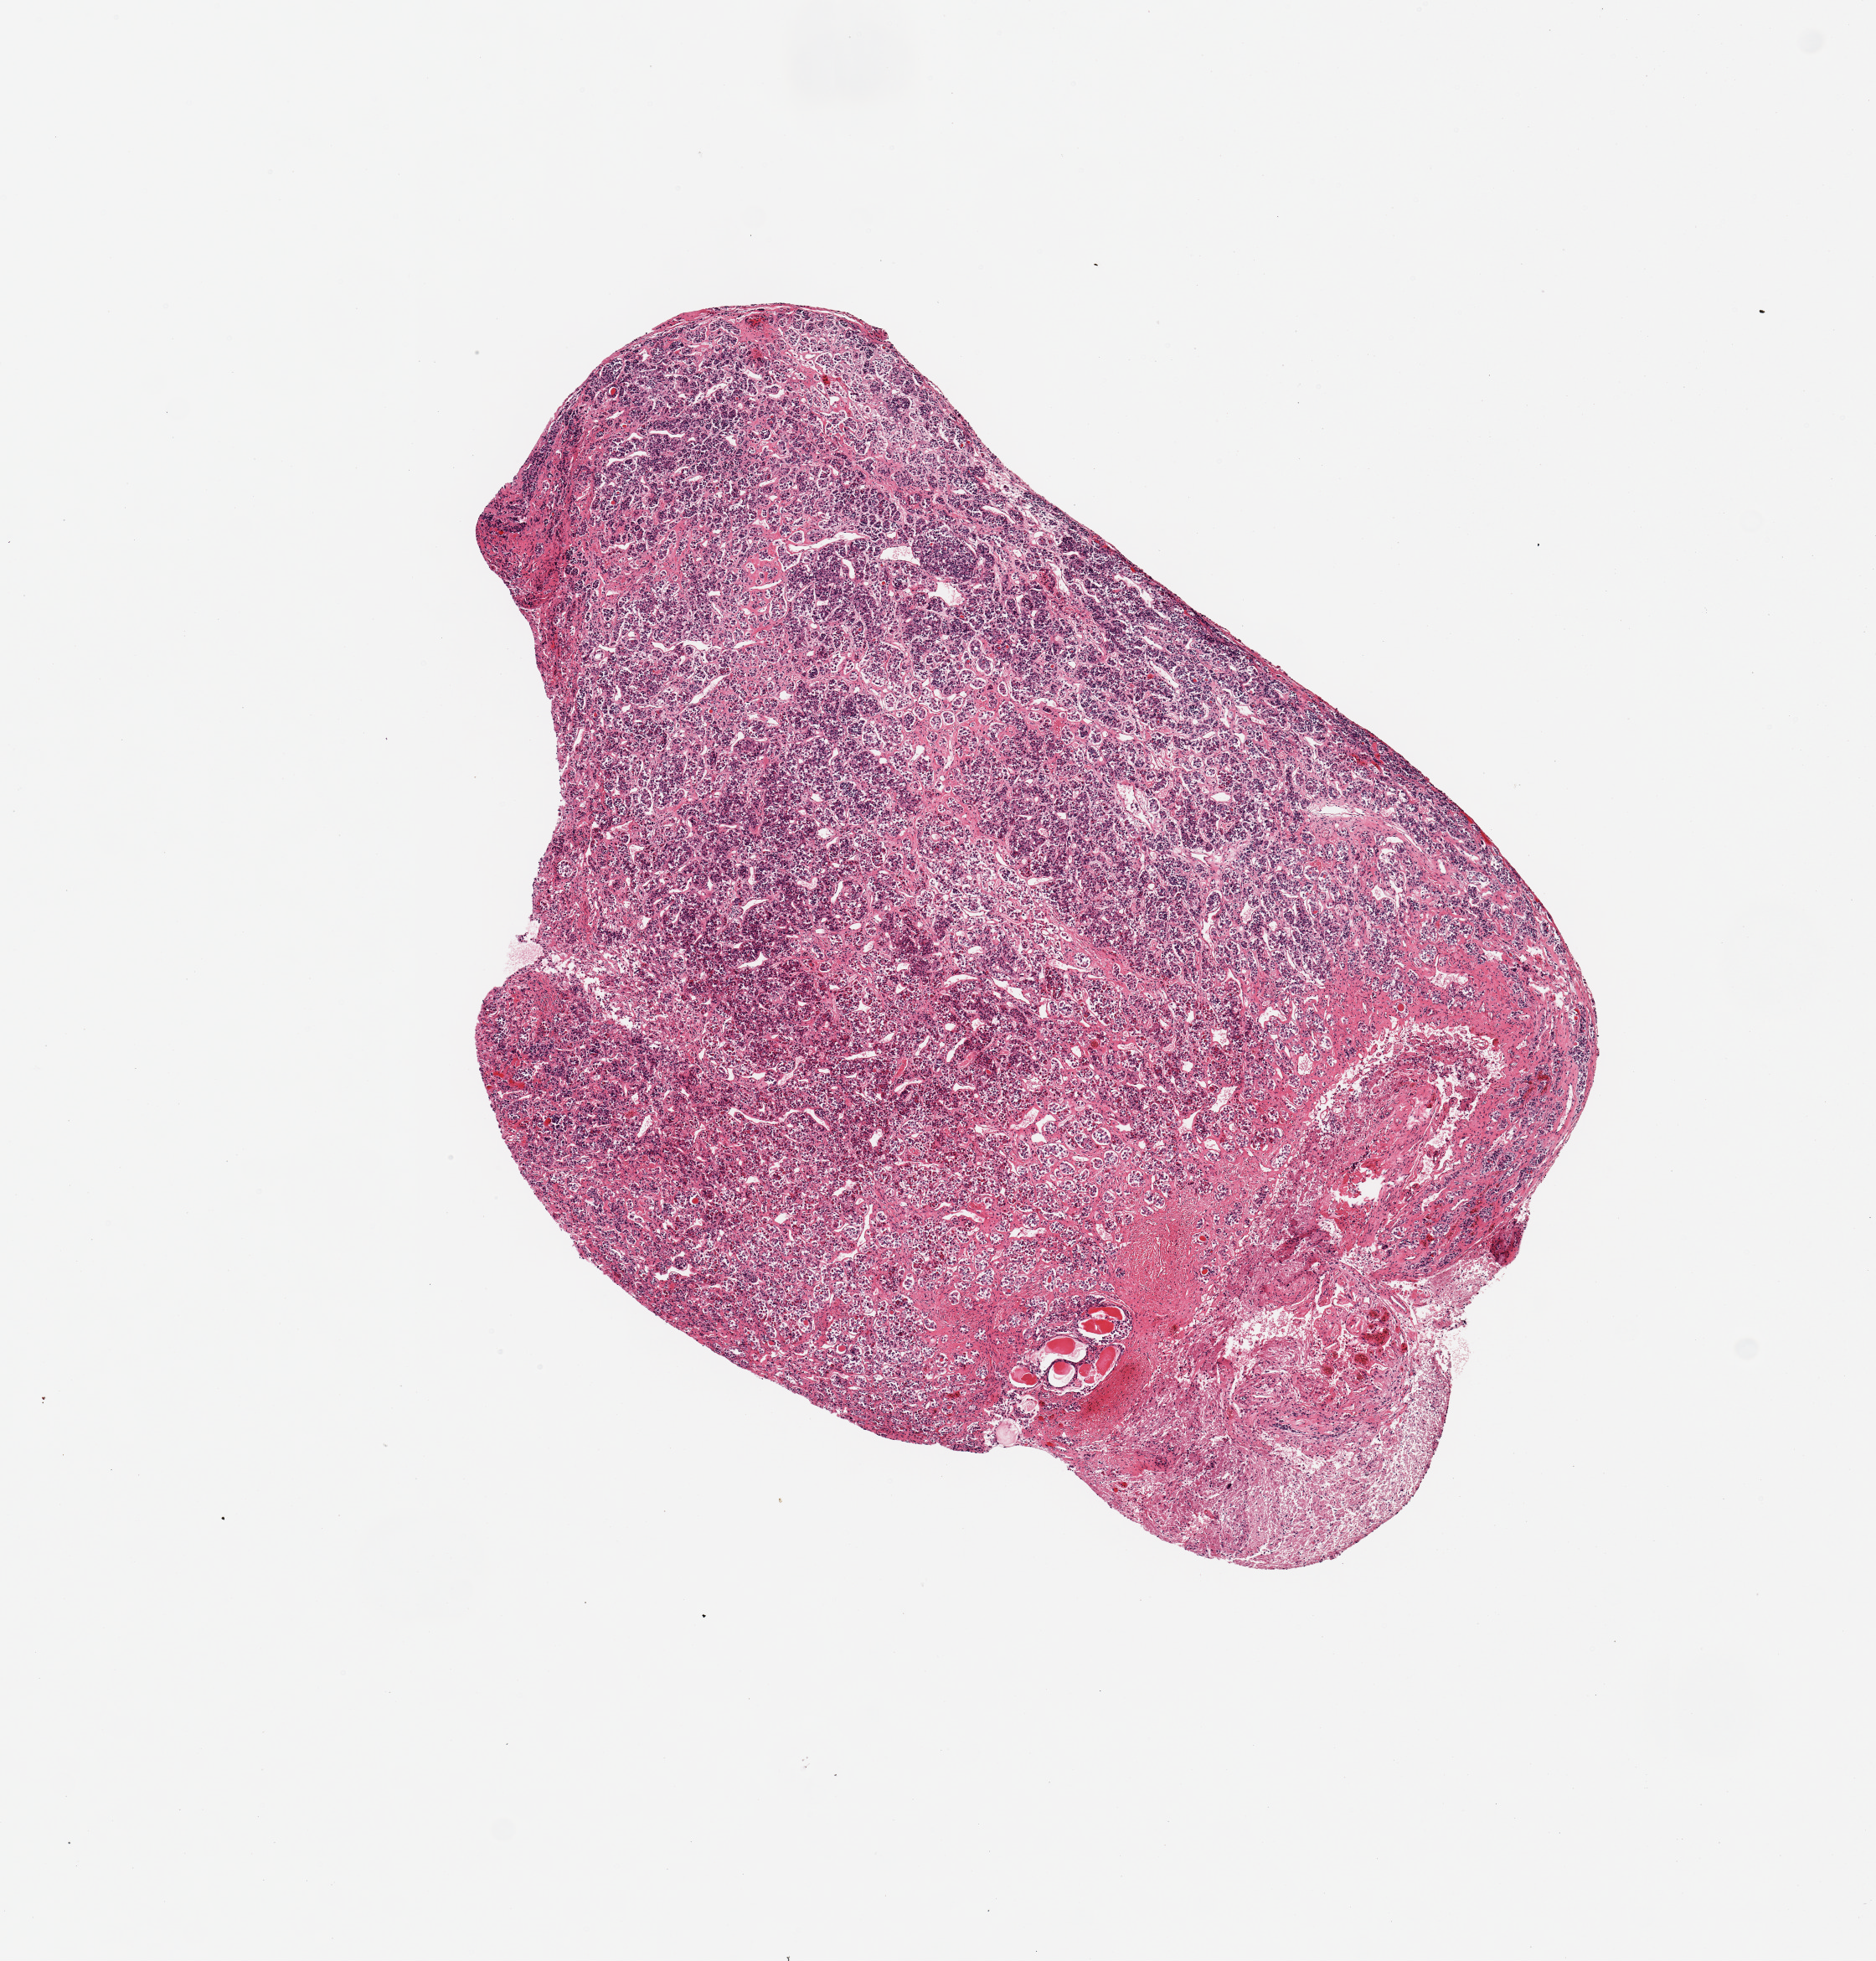
Digitized H&E-stained section, whole scanned area (about 8.9 x 9.3 mm) shown as a low-resolution overview; PAXgene-fixed, paraffin-embedded tissue; sampled site (target tissue): pituitary; donor tissue sample. Donor: male.
Reviewer comment on this tissue sample: 1 piece; mostly anterior.